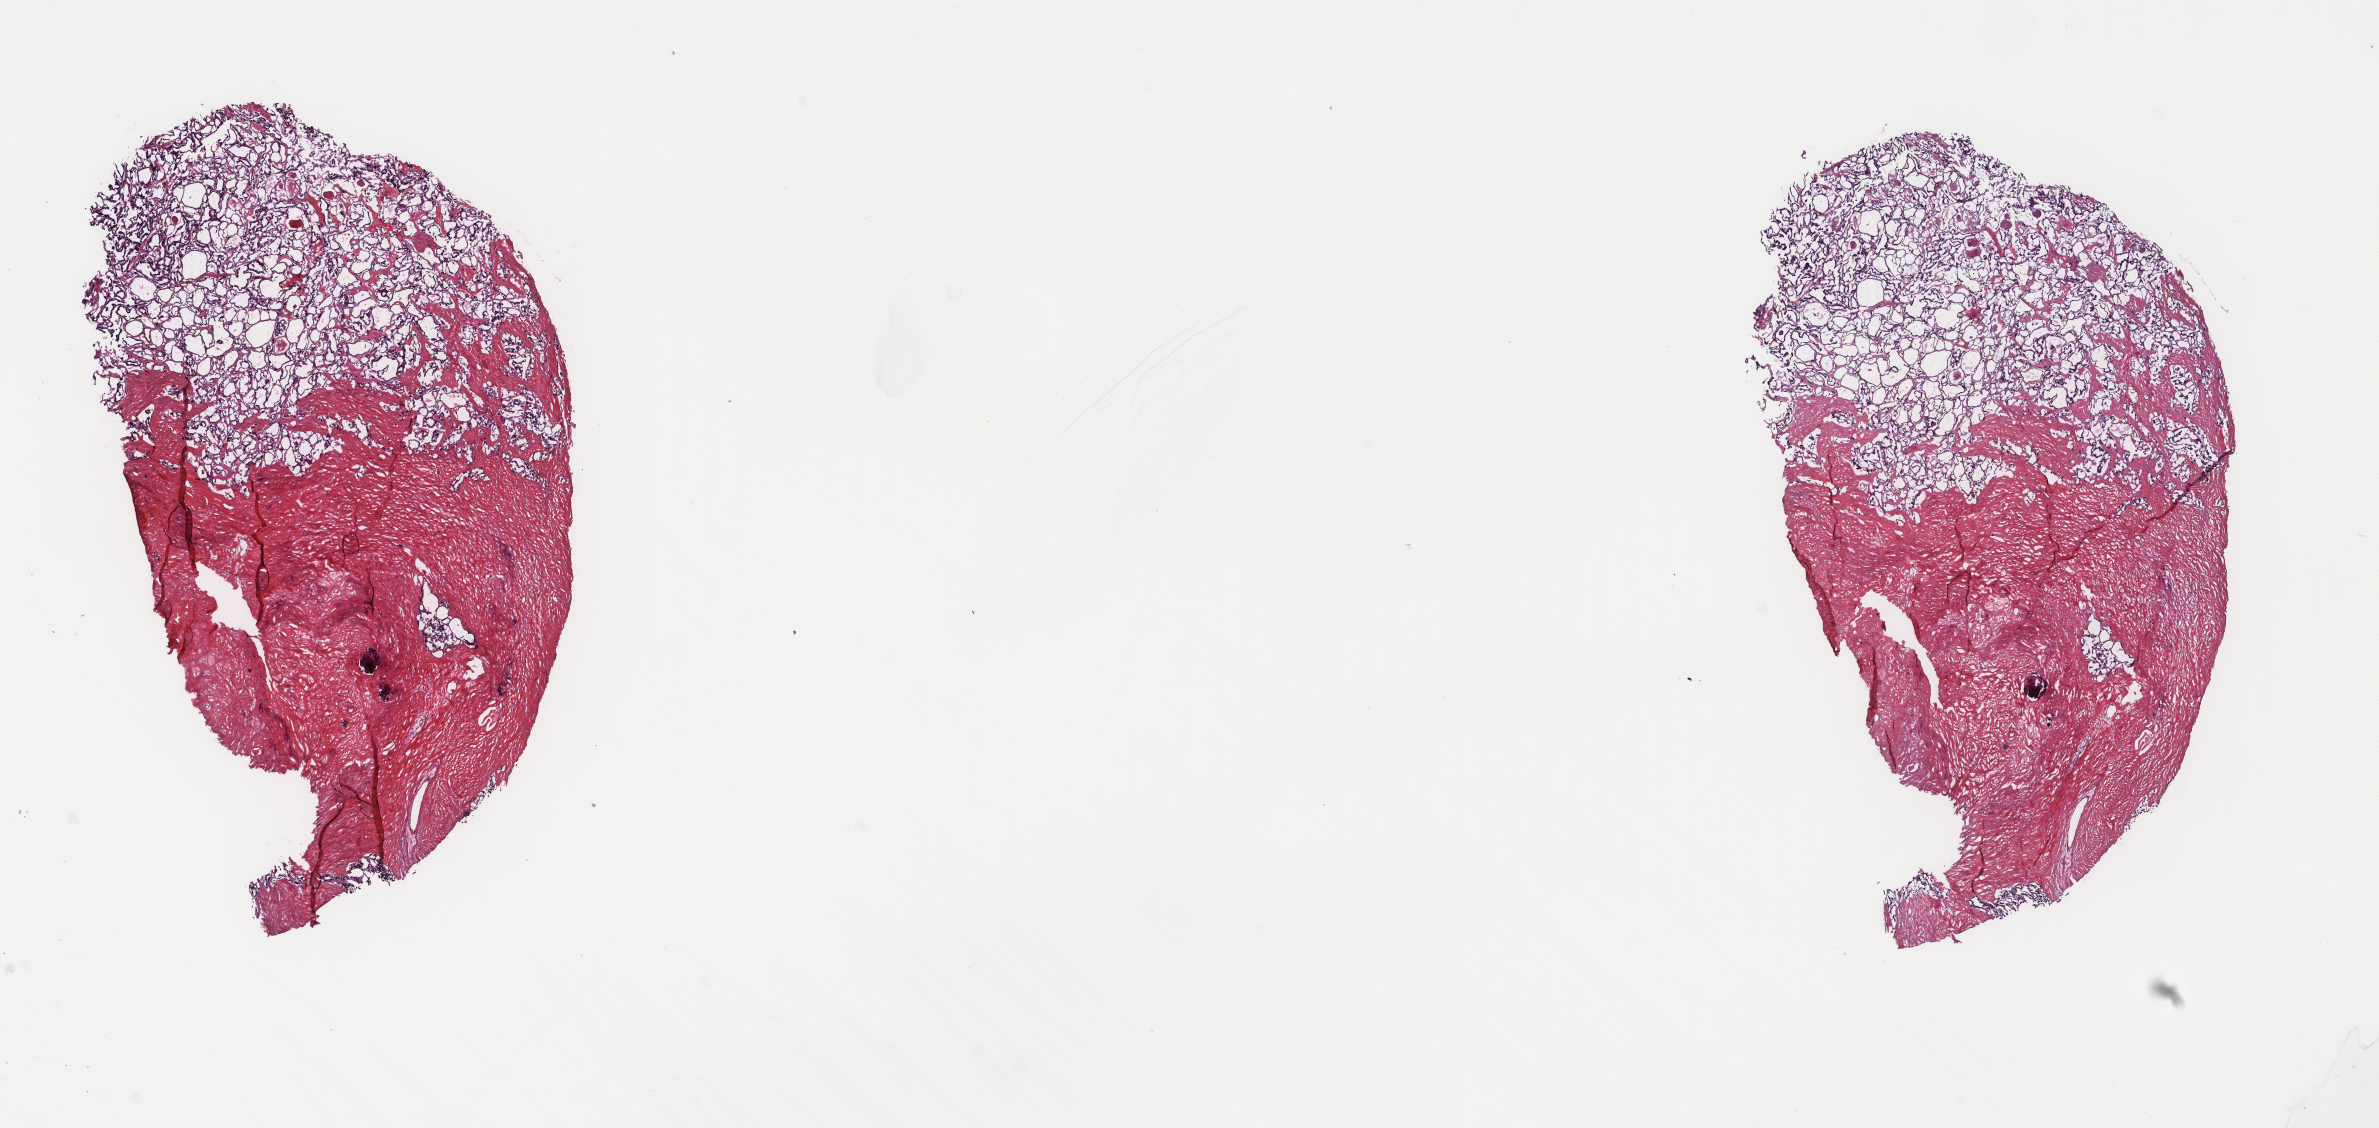
Digitized Hematoxylin and eosin (H&E) stained tissue section (whole slide), low-resolution overview of the scanned area, about 18.9 x 9.0 mm (acquisition: 40x scan), frozen section from the top of the tissue portion, sample: primary tumour, thyroid. Patient: male, age at initial diagnosis 51 years. Composition of this section per pathologist review: tumour cells 75%, tumour nuclei 95%, normal cells 0%, stromal cells 25%, necrosis 0%. Infiltration values recorded for this section: lymphocyte infiltration 0%, monocyte infiltration 0%, neutrophil infiltration 0%.
AJCC pathologic stage: III (6th edition). Histologic diagnosis: Papillary adenocarcinoma, NOS (thyroid gland). Laterality: right. Lymph nodes positive (case pathology): 20 of 85 examined.